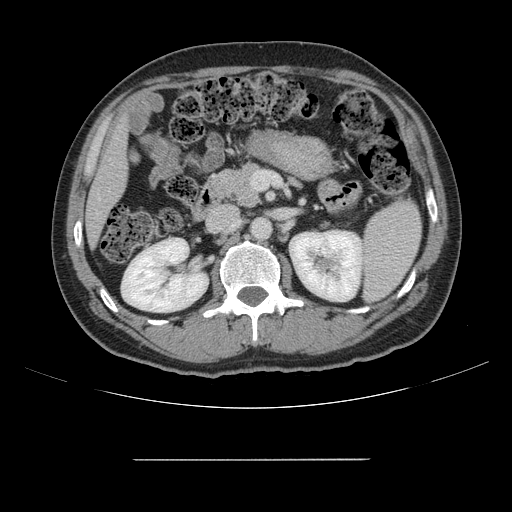
Contrast-enhanced abdominal CT, one axial slice; slice 65 of 164 in the series (ordered by position); intravenous contrast given; soft-tissue window (W 400 / L 40 HU); 2.5 mm slice thickness; 512 × 512 image matrix. Male patient, age 54 years. From the clinical record (not read from this slice): diagnosis: colorectal cancer liver metastases, imaged before liver resection; multiple liver metastases: yes.
Structures marked on this image (outlined manually by an expert reader):
- liver: bounding box (x1, y1, x2, y2) in pixels: (87, 125, 126, 241)
- planned liver remnant (the part of the liver to remain after resection): (87, 124, 126, 242)